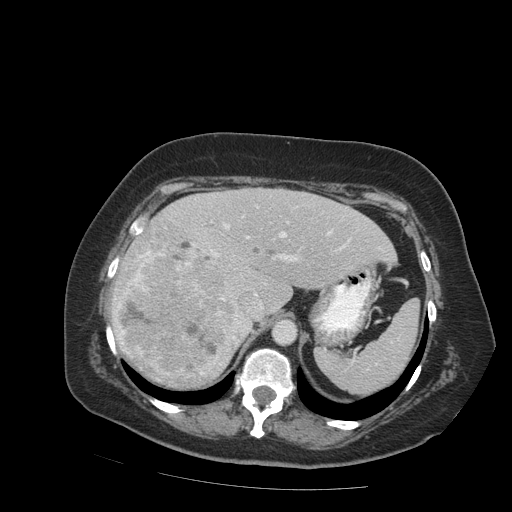
Contrast-enhanced abdominal CT (liver protocol), one axial slice. Slice 60 of 99 in the series (ordered by position). 140 kVp. Soft-tissue window (W 400 / L 40 HU). 2.5 mm slice thickness. 512 × 512 image matrix, field of view 400 × 400 mm. From the clinical record (not read from this slice): diagnosis: hepatocellular carcinoma (patient treated with transarterial chemoembolisation; whether this scan precedes or follows treatment is not stated here); TNM stage (as recorded): Stage-IVB.
Annotated regions visible in this slice (semi-automatic segmentation, software-assisted and operator-edited):
- abdominal aorta: bounding box <273,320,296,344> (left, top, right, bottom; pixels)
- liver parenchyma outside the tumour (the mass and vessels are separate outlines, so this box may not span the whole liver): <110,188,396,386>
- mass: <115,225,249,388>
- liver vessels: <113,207,350,314>